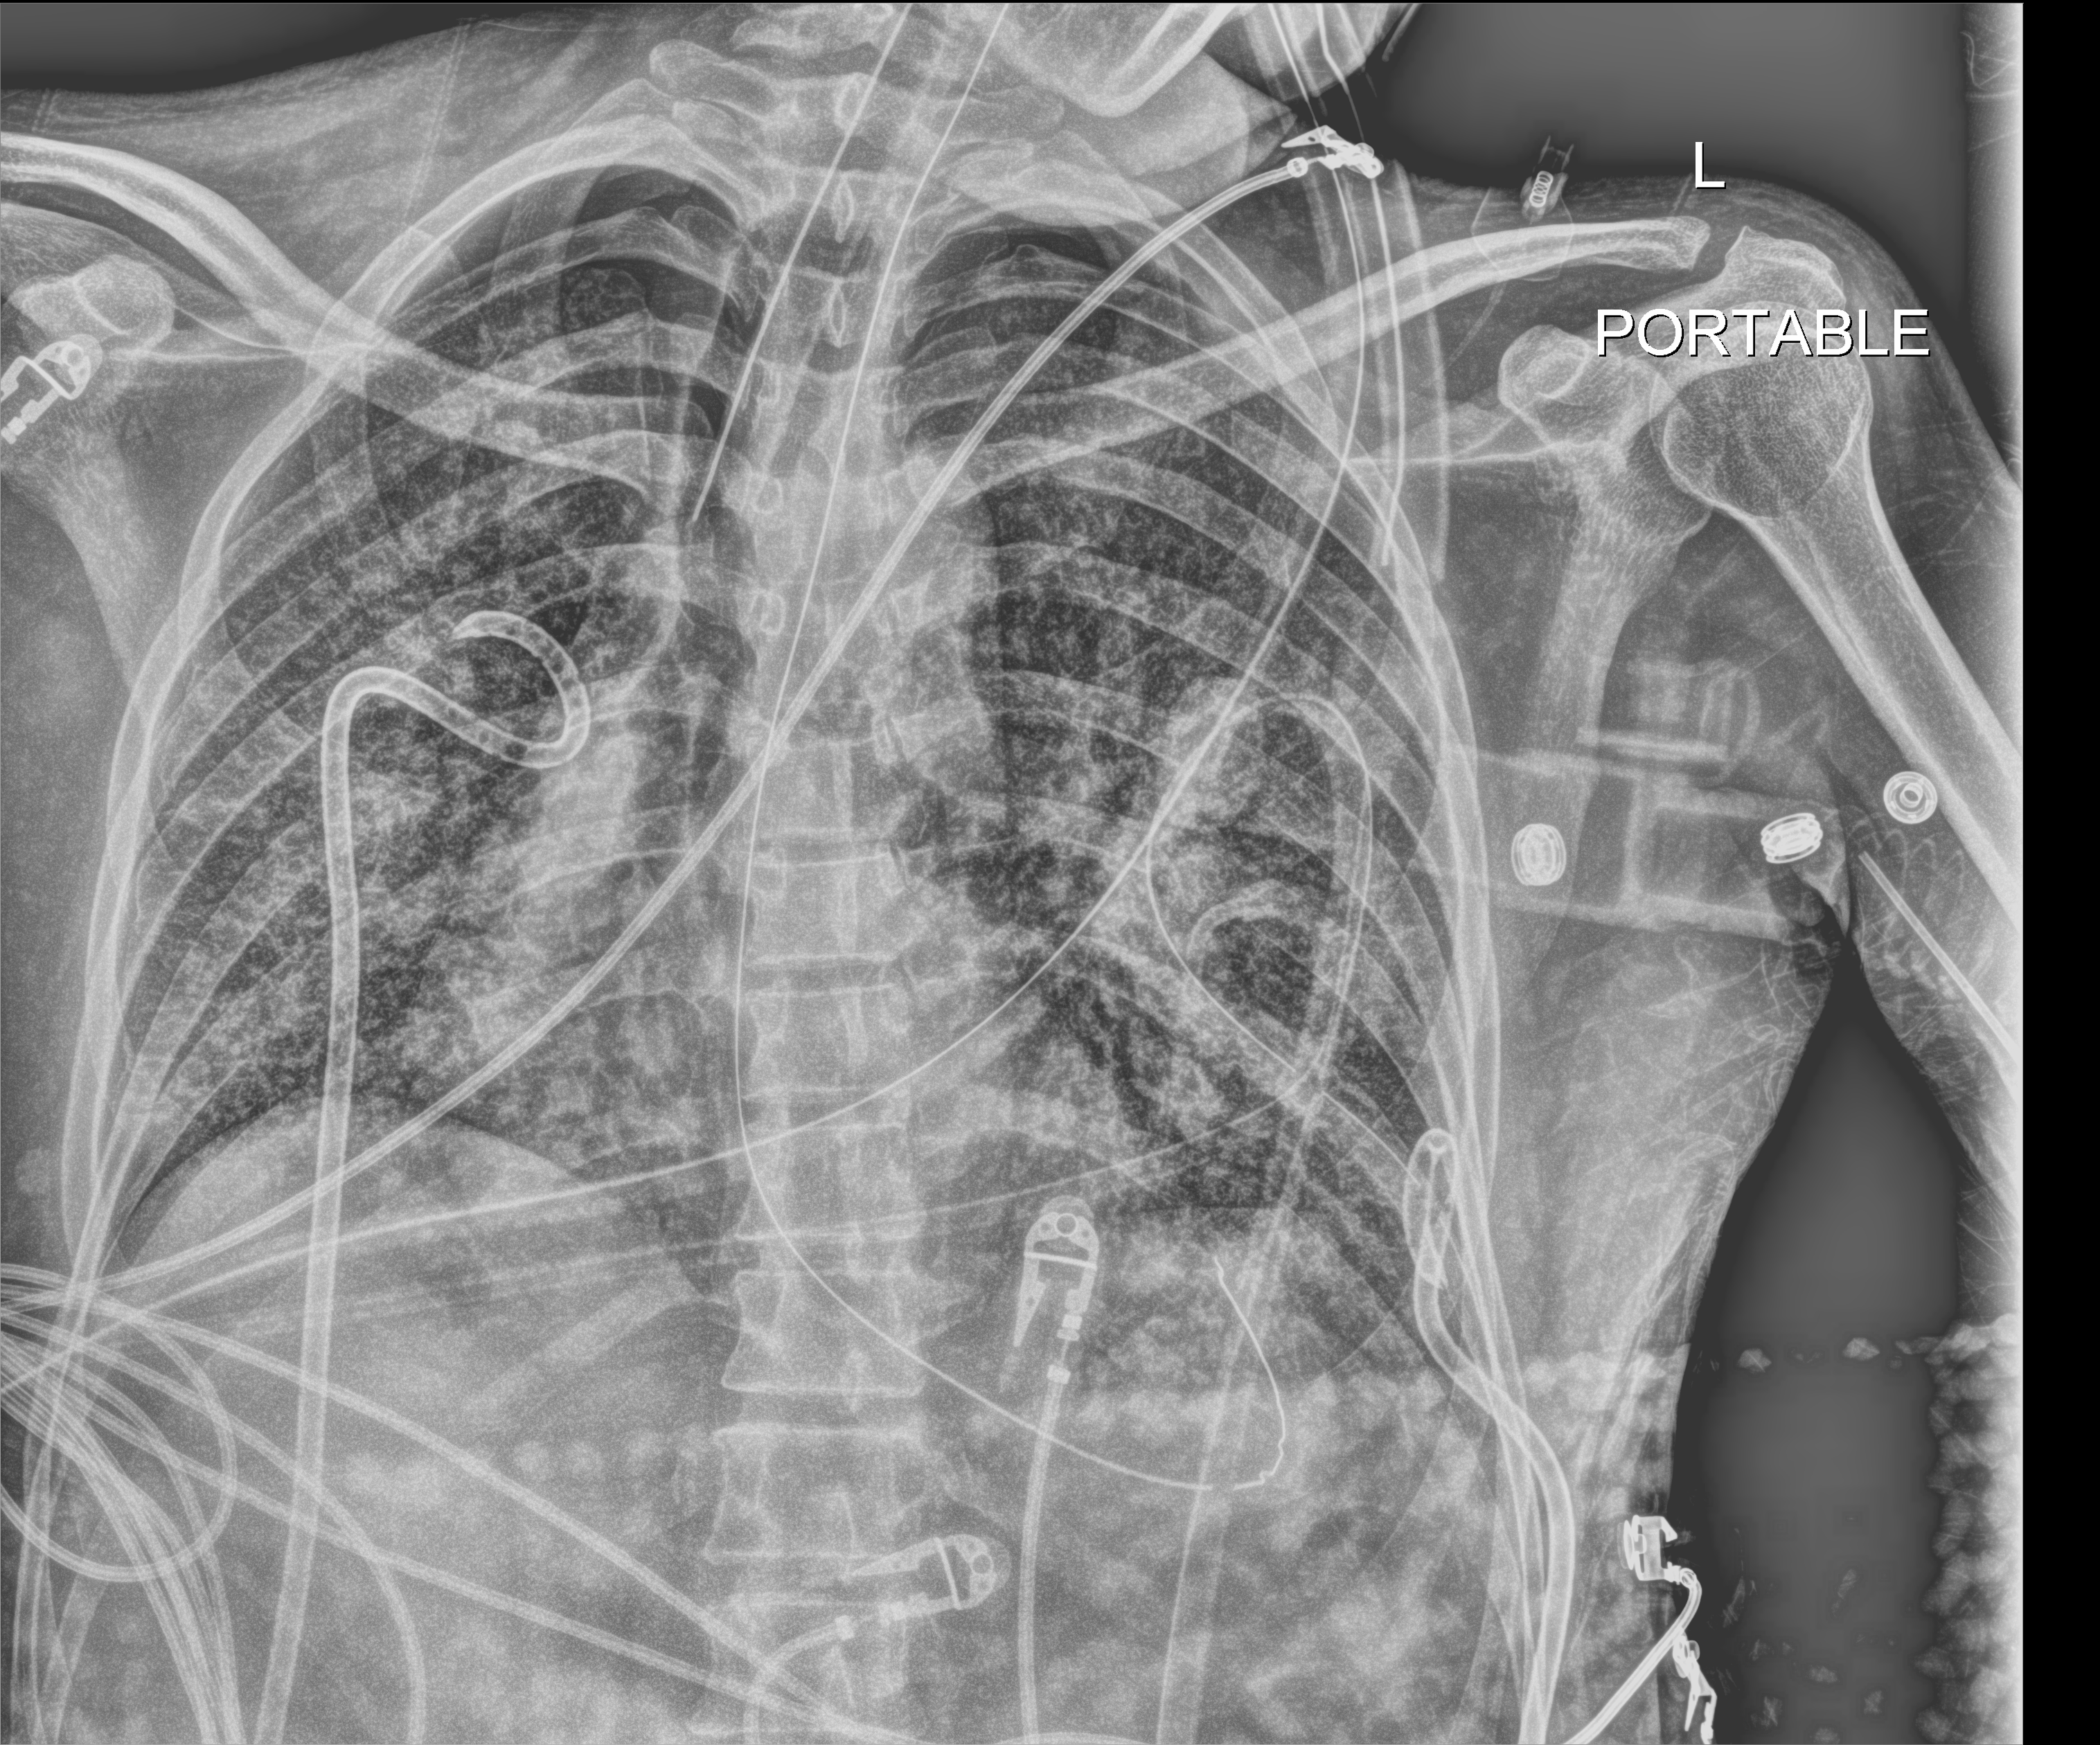
Chest radiograph (digital radiography), anteroposterior (AP) projection. Adult patient hospitalised with COVID-19, age 18–59 years.
From the hospital-stay record, not from the radiograph (when in the stay this image was taken is not recorded): diabetes (admission record): no; mechanically ventilated during this hospital stay: yes.